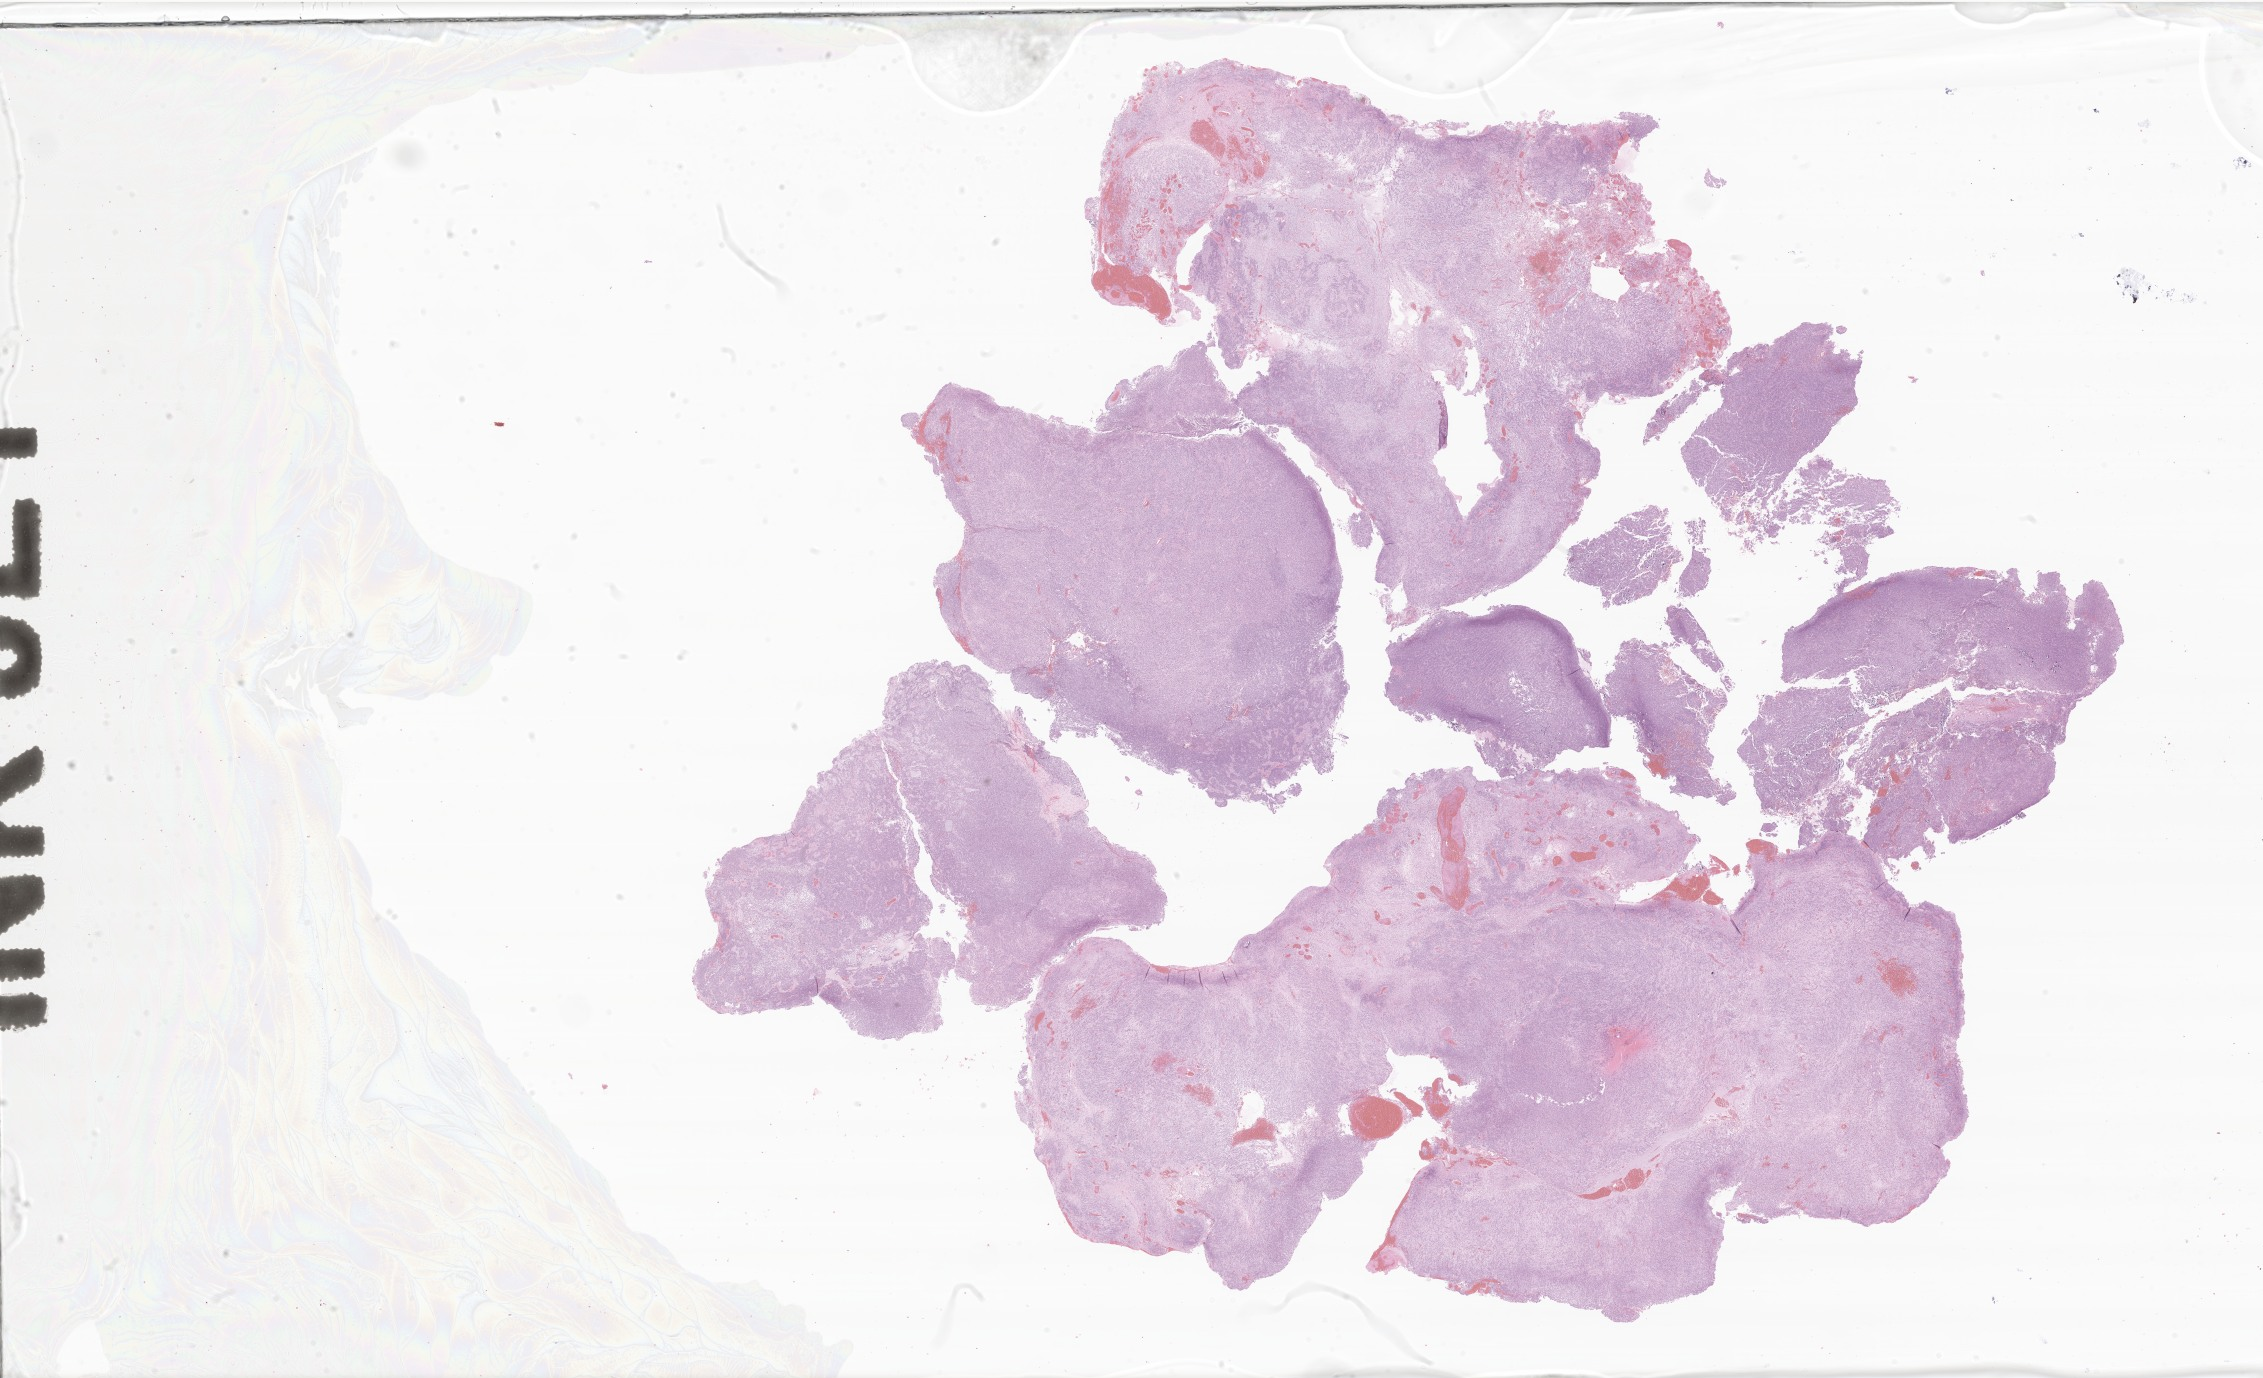
Whole-slide image, H&E stain of tumor tissue from the brain — low-resolution overview of the scanned area, about 38.2 x 23.2 mm; FFPE section. Patient: female, age 130 months (10 years 10 months).
Recorded diagnosis: Neoplasm, malignant.